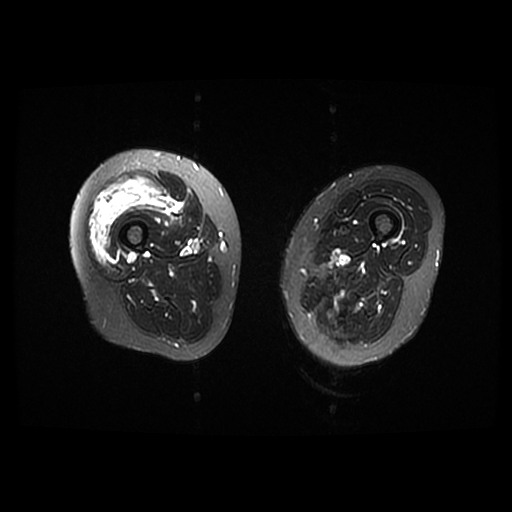
MRI of an extremity soft-tissue mass, one axial slice; position 11 of 42 along the scan axis; T2-weighted fat-saturated; 512 × 512 image matrix, field of view 440 × 440 mm. Female patient. From the clinical record (not read from this slice): histological type: pleiomorphic undifferentiated sarcoma; grade: high; site of the primary tumour: right quadricep.
Annotated regions visible in this slice (manually delineated by an expert):
- gross tumour volume including surrounding oedema: box from (x=89, y=177) to (x=176, y=261) px